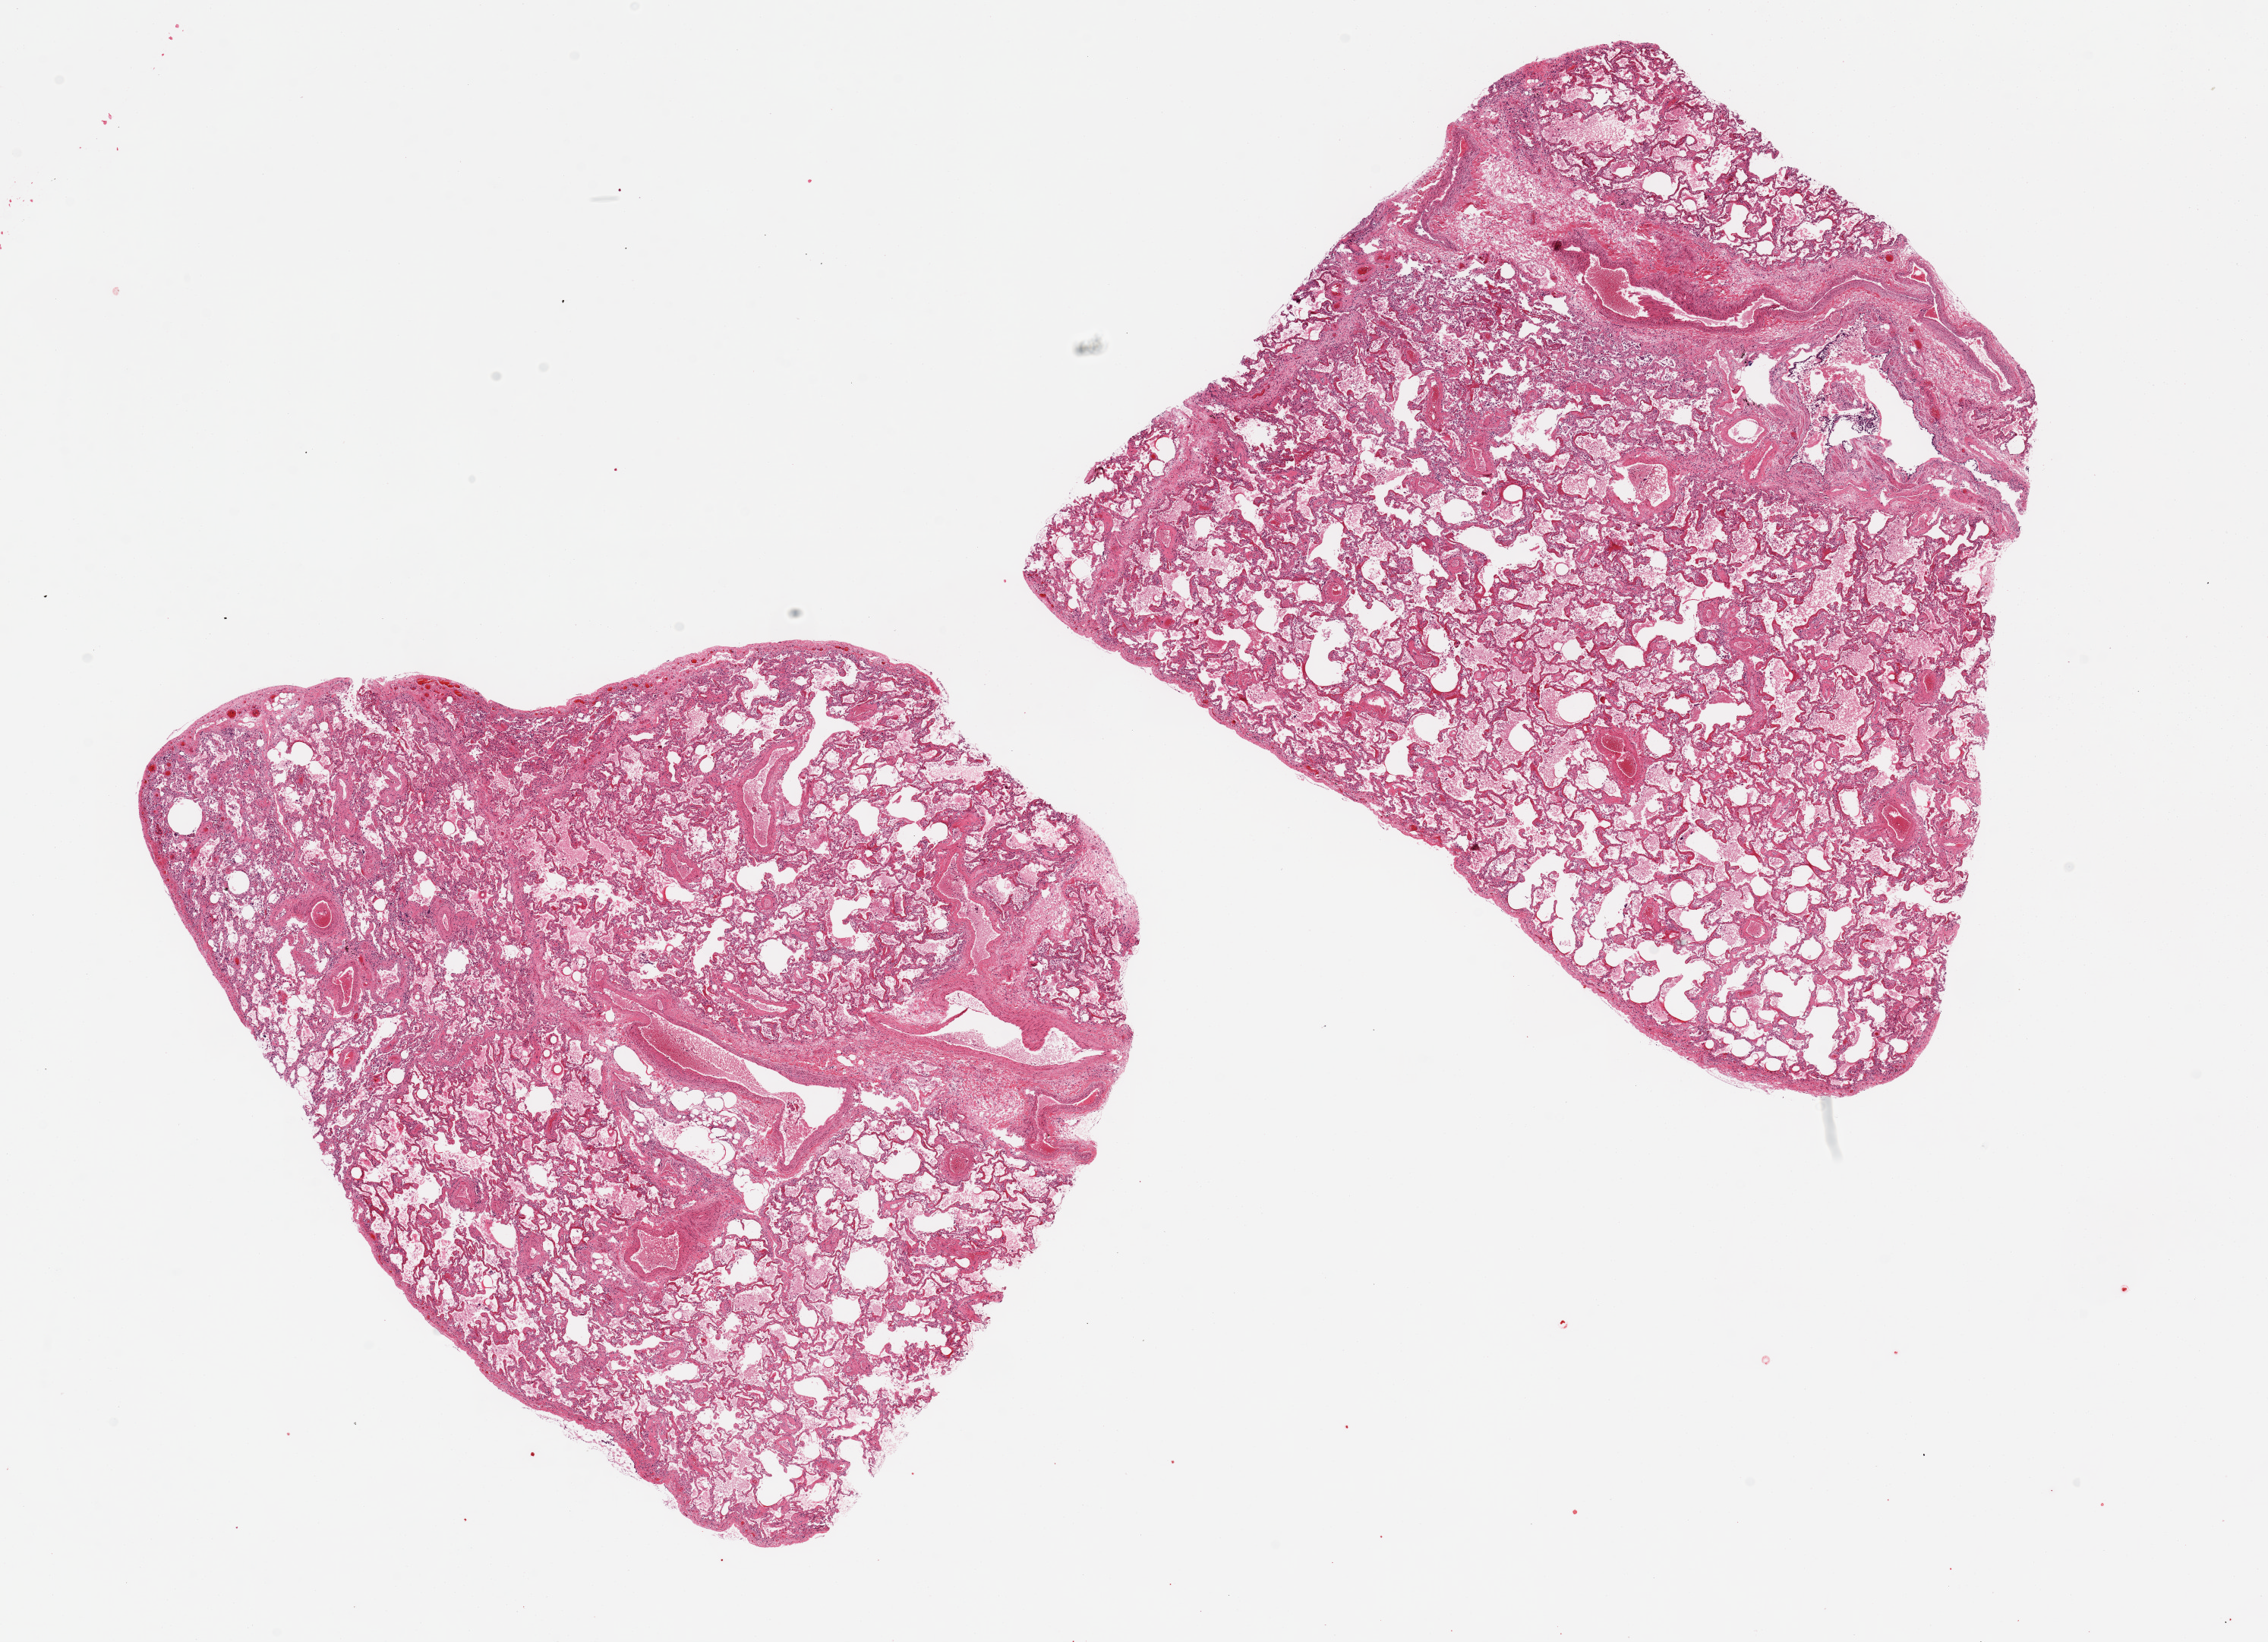
Digitized H&E-stained section — a low-resolution overview of the entire scanned area, about 23.6 x 17.1 mm (from a 20x scan). PAXgene-fixed paraffin-embedded (PFPE) section. Target tissue: lung. Tissue donor sample. Female donor.
- reviewer comment on this tissue sample: 2 pieces 10x8 mm each; hyalin membranes; small vessel sclerosis; no pneumonia